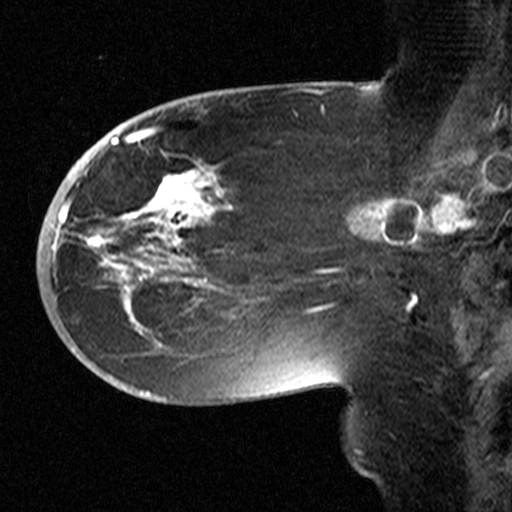
Breast MRI (dynamic contrast-enhanced), one sagittal slice; slice 18 of 44 in the series (ordered by position); dynamic contrast-enhanced study with each time point stored as its own series, time point 2 of 3 at this slice position (early post-contrast, ordered by acquisition time); 1.5 T; TE 4.5 ms, TR 11 ms; 3.27 mm slice thickness; 512 × 512 image matrix, field of view 200 × 200 mm. Patient: female, 53 years. Case-level facts recorded for this patient, not image findings: setting: breast cancer imaged before/during neoadjuvant chemotherapy; receptor status: HR-positive, HER2-negative.
Outlined on this slice (semi-automatically segmented with operator editing):
- analysis volume of interest (the breast-tissue region the enhancement analysis was run in; not a lesion): bounding box [x1, y1, x2, y2] px = [58, 154, 311, 367]
- tumour enhancement mask (voxels above the 90 % enhancement threshold inside the analysis volume of interest): [60, 171, 310, 330]